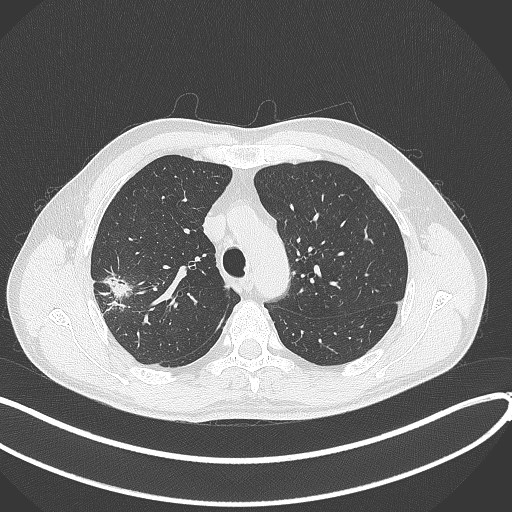
Chest CT, one axial slice; position 310 of 381 along the scan axis; lung window (W 1500 / L -600 HU); 512 × 512 image matrix, field of view 400 × 400 mm. Male patient, age 62 years. Case-level facts recorded for this patient, not image findings: clinical TNM (as recorded): T1c N0 M0; histopathological grade: G2-3.
Outlined on this slice (rectangle marked by the reading radiologist):
- lung tumour (recorded histology: adenocarcinoma): bounding box (x1, y1, x2, y2) in pixels: (102, 268, 131, 300)